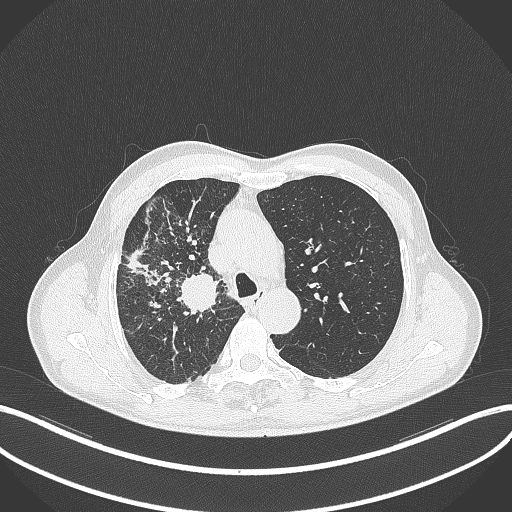
Chest CT, one axial slice; slice 345 of 490 in the series (ordered by position); reconstruction kernel B70f; lung window (W 1500 / L -600 HU); 1 mm slice thickness; 512 × 512 image matrix, field of view 400 × 400 mm. Male patient, age 69 years. Case-level facts recorded for this patient, not image findings: clinical TNM (as recorded): T2a N0 M0.
Structures marked on this image (bounding box drawn by a radiologist):
- lung tumour (recorded histology: adenocarcinoma): bounding box <177,269,224,315> (left, top, right, bottom; pixels)